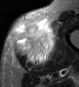
MRI of an extremity soft-tissue mass, one axial slice; position 15 of 45 along the scan axis; STIR; MR volume resampled by the dataset authors to the PET/CT grid (not the native acquisition matrix); 3.27 mm slice thickness; 79 × 87 image matrix. Male patient. From the clinical record (not read from this slice): histological type: pleiomorphic leiomyosarcoma; grade: high; site of the primary tumour: left thigh.
Annotated regions visible in this slice (expert contour drawn on MRI and transferred to this co-registered scan by the dataset authors):
- gross tumour volume including surrounding oedema: bounding box [x1, y1, x2, y2] px = [13, 18, 58, 67]
- gross tumour volume (mass): [13, 20, 55, 63]